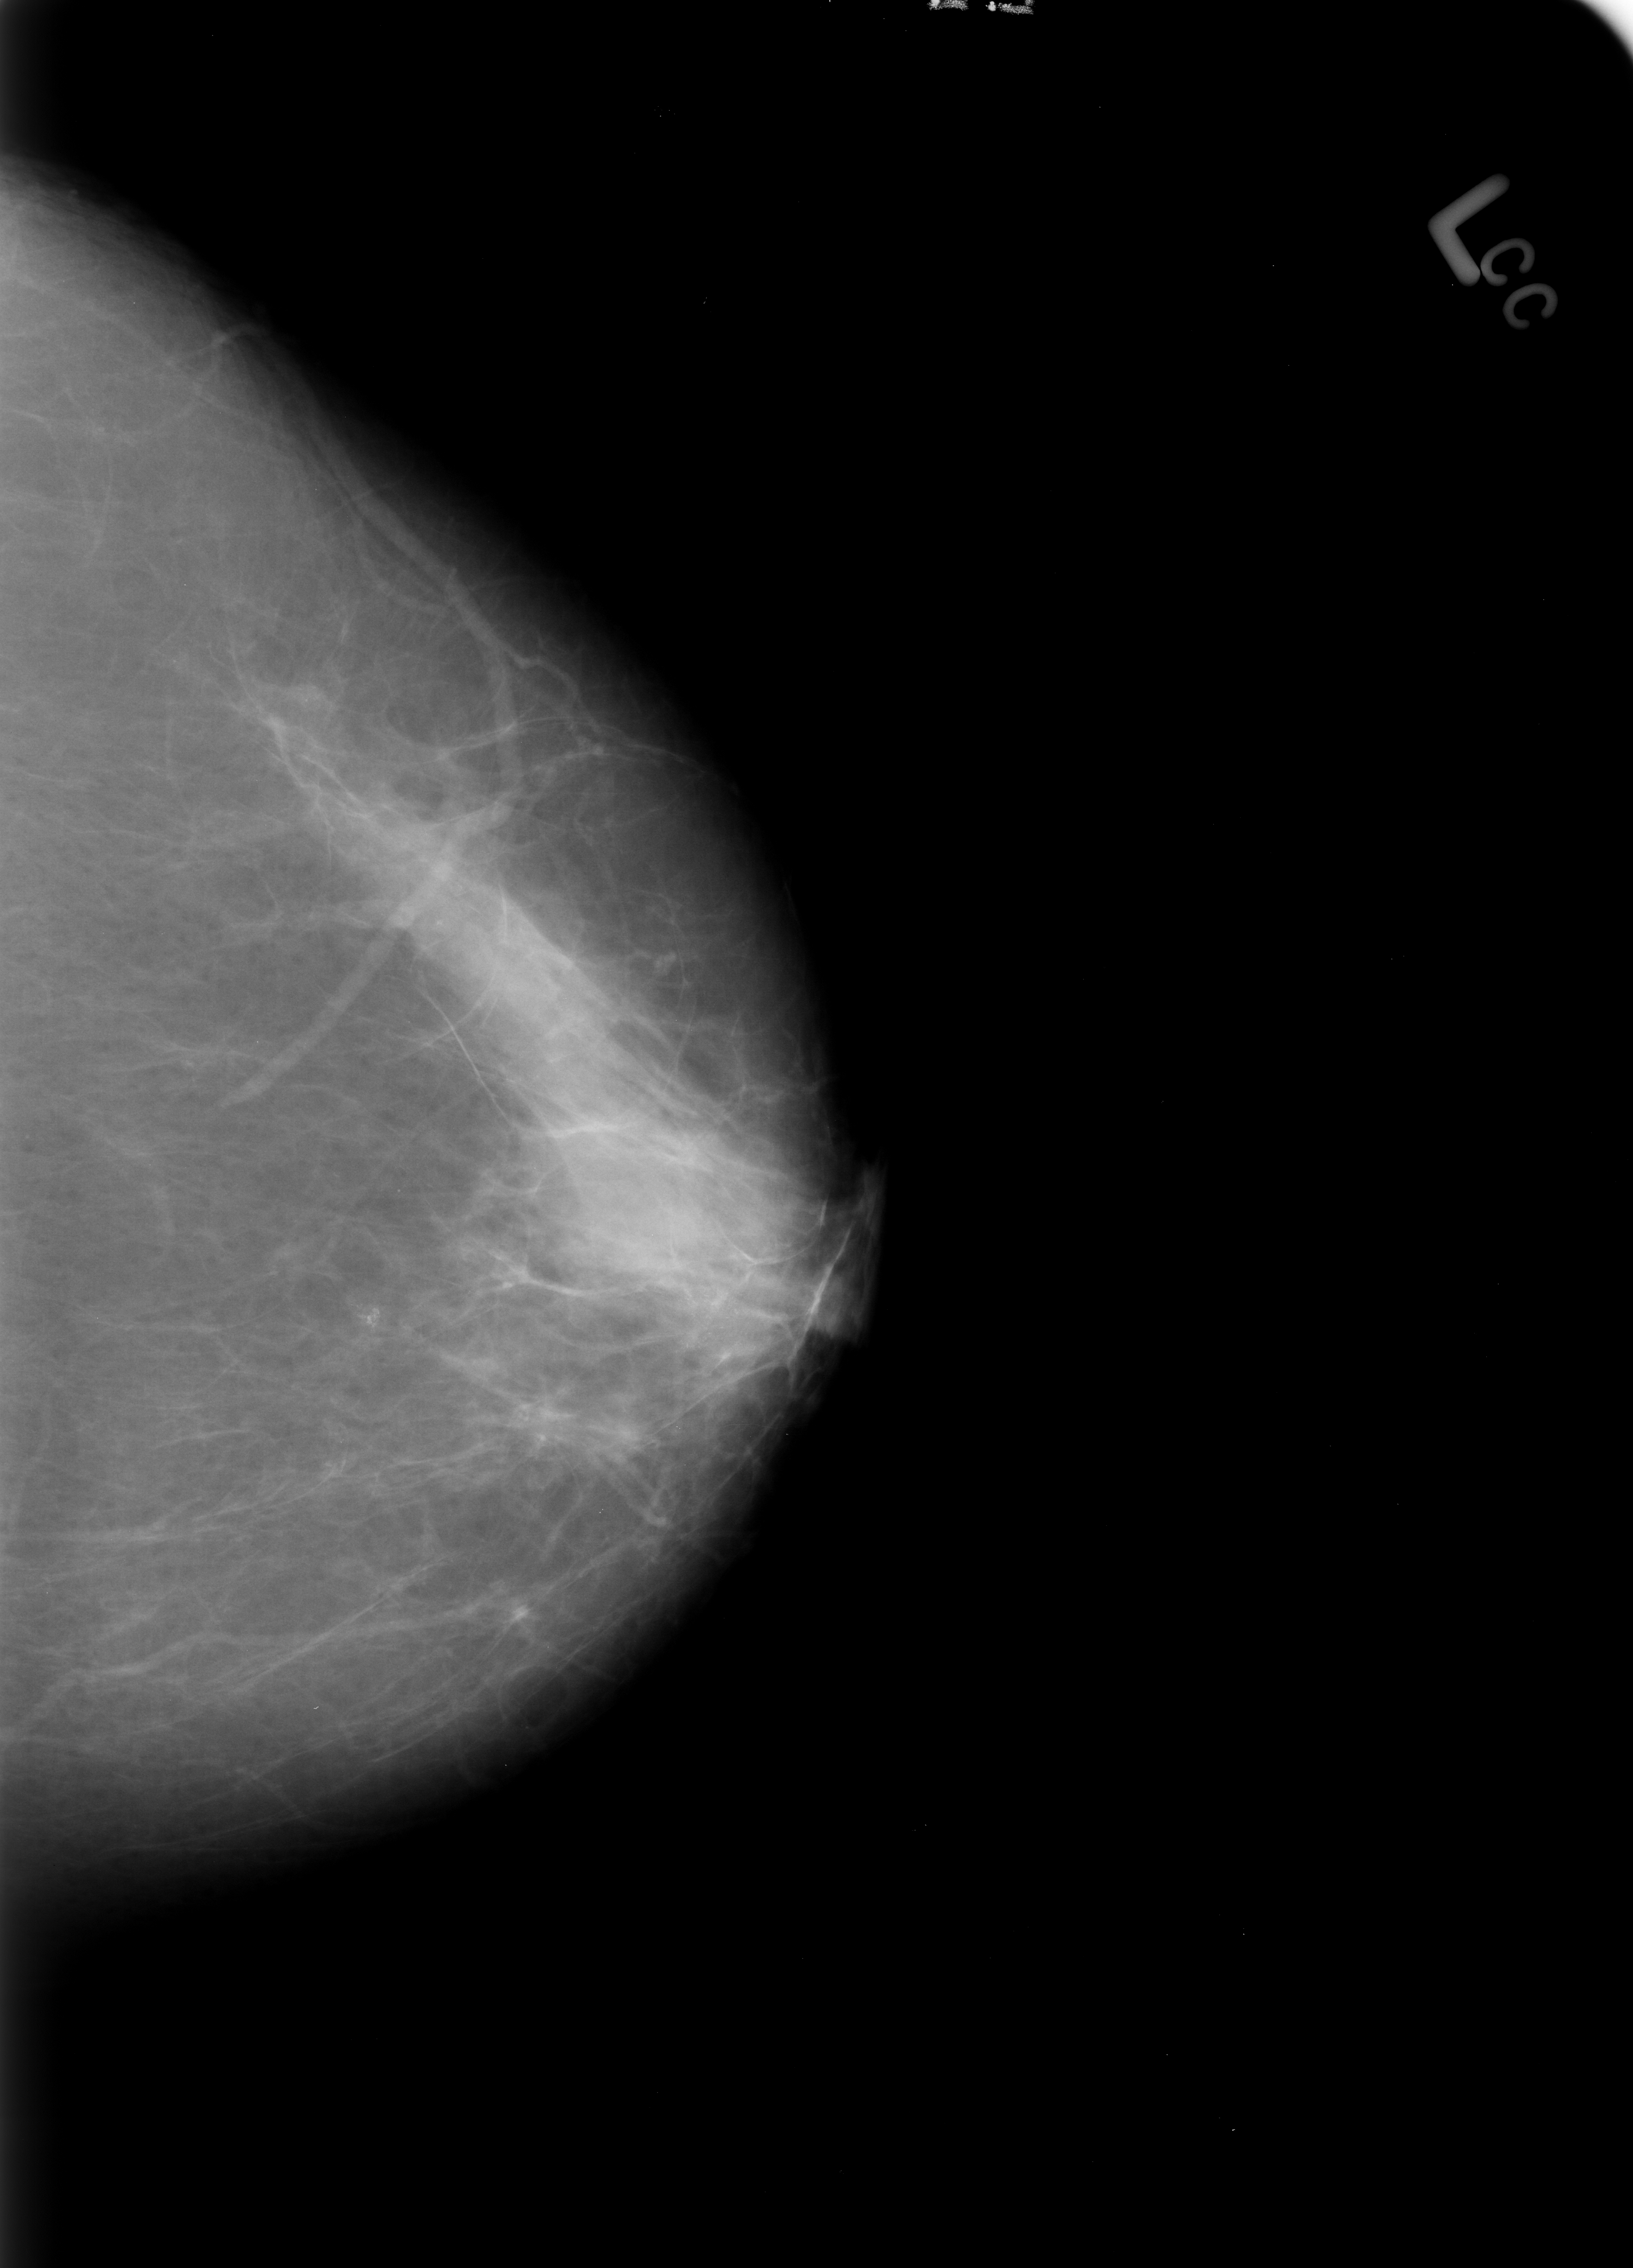
Digitized screen-film mammogram. Left breast. Craniocaudal (CC) view. BI-RADS breast density category 2 (scale 1–4). 1633 × 2268 image matrix.
Expert-marked regions of interest on this image (one box per marked abnormality):
- Finding 1 of 2: calcifications, morphology pleomorphic, distribution clustered; BI-RADS assessment category 4; subtlety rating 4 on a 1 (subtle) to 5 (obvious) scale; pathology result (as recorded, not read from the image): benign: box from (x=337, y=1279) to (x=404, y=1356) px
- Finding 2 of 2: calcifications, morphology pleomorphic / fine linear branching, distribution clustered; BI-RADS assessment category 4; subtlety rating 2 on a 1 (subtle) to 5 (obvious) scale; pathology result (as recorded, not read from the image): benign: (x=647, y=1272)–(x=755, y=1360)